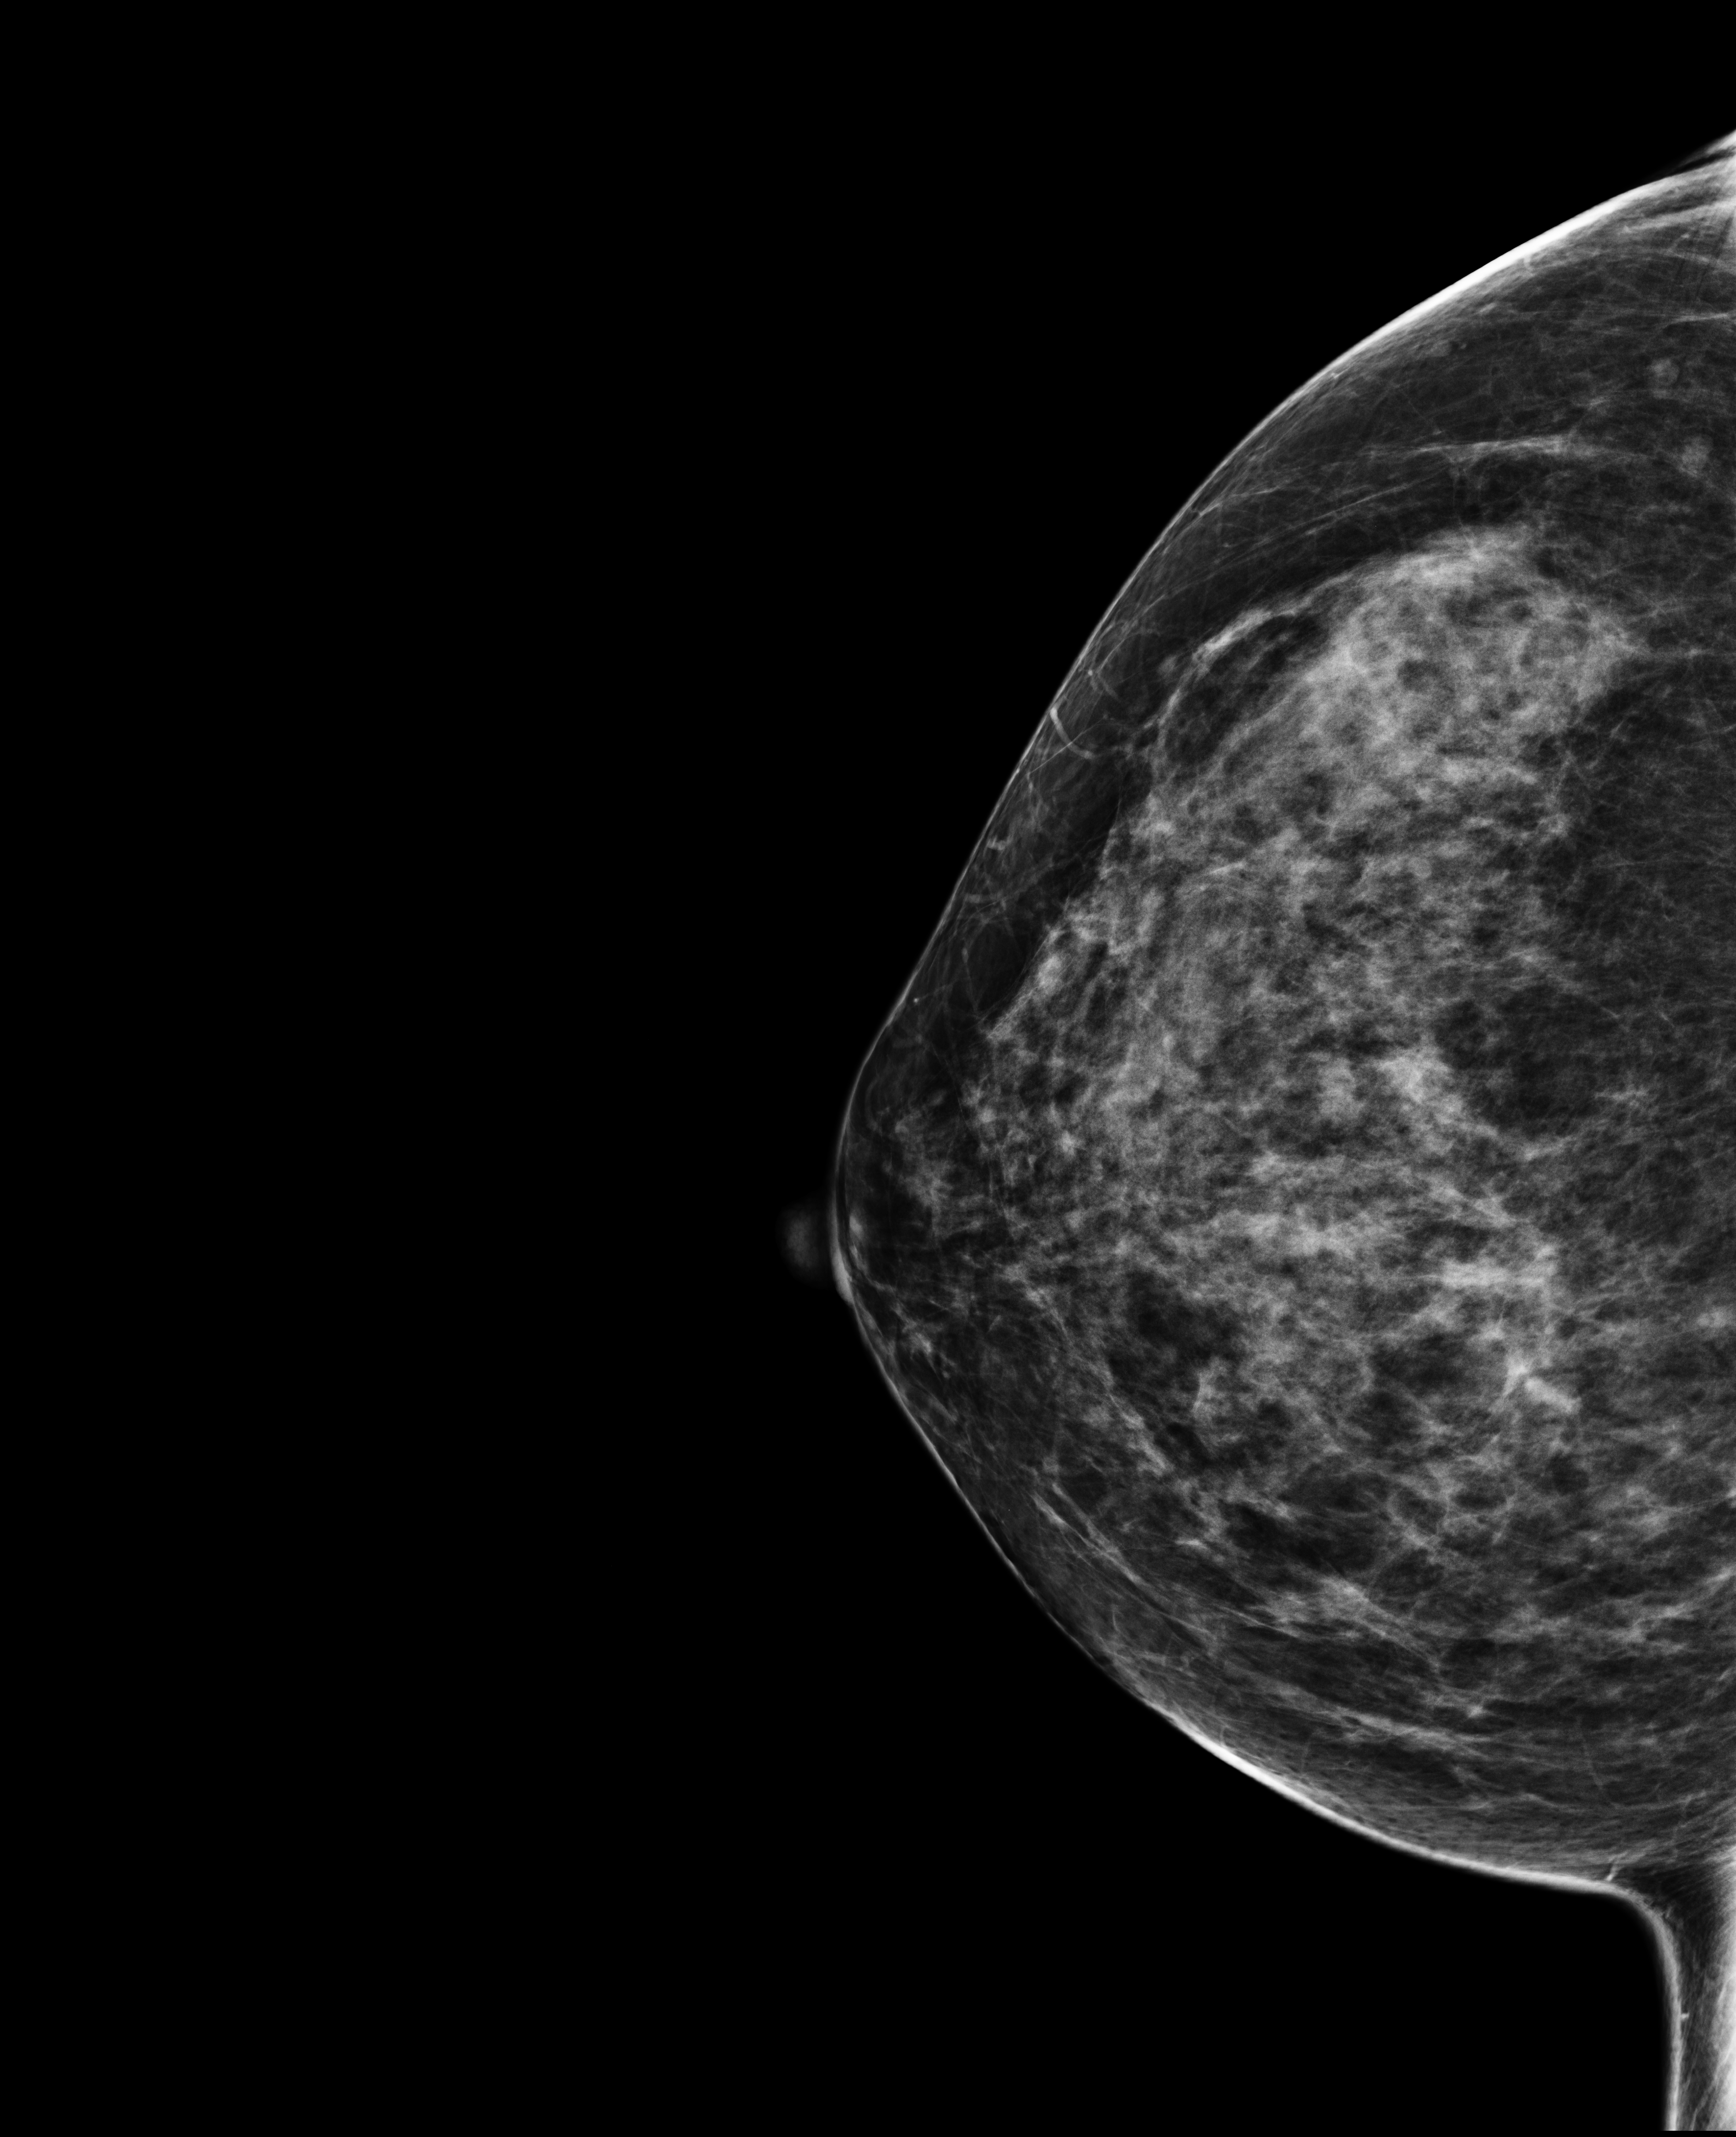
Screening examination. Patient: female, 47 years.
Image type: full-field digital mammogram. Breast: right. Projection: CC view.